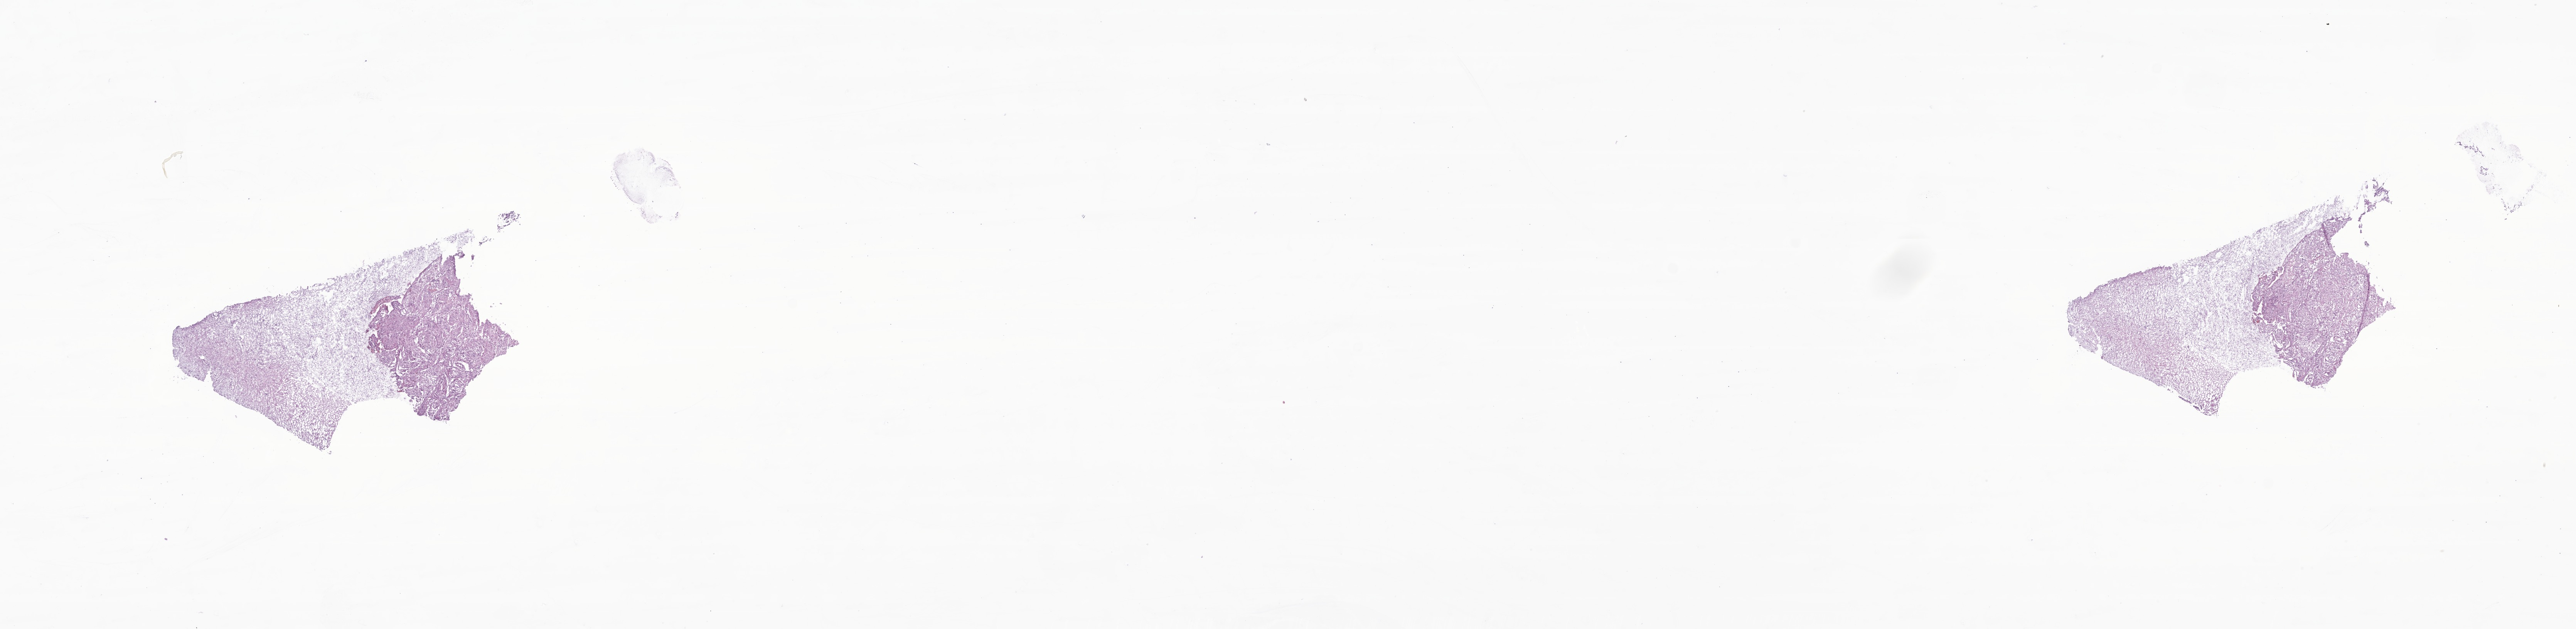
Whole-slide image, H&E stain of tumor tissue from the brain — whole scanned area (about 28.2 x 6.9 mm) shown as a low-resolution overview; frozen section. Patient female; age 42 months (3 years 6 months).
• recorded diagnosis: Pilocytic astrocytoma